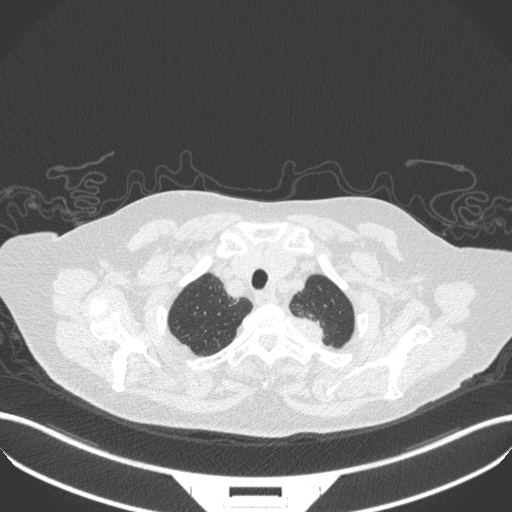
Chest CT, one axial slice. Slice 309 of 353 in the series (ordered by position). 100 kVp. Lung window (W 1500 / L -600 HU). 1 mm slice thickness. 512 × 512 image matrix, field of view 400 × 400 mm. Patient: female, 81 years. Case-level facts recorded for this patient, not image findings: clinical TNM (as recorded): T2a N0 M0.
Structures marked on this image (bounding box drawn by a radiologist):
- lung tumour (recorded histology: adenocarcinoma): bounding box [x1, y1, x2, y2] px = [289, 312, 334, 353]